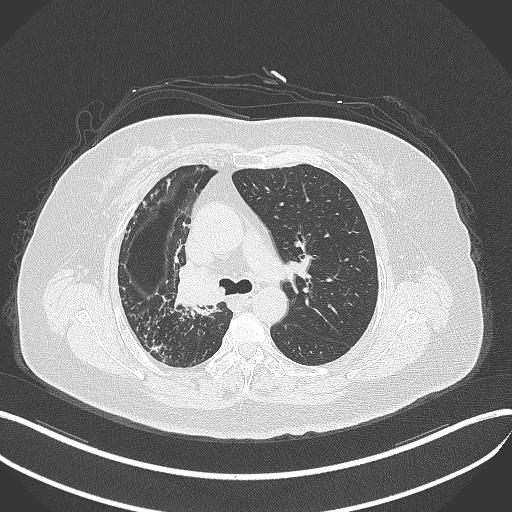
Chest CT, one axial slice. Position 236 of 376 along the scan axis. Lung window (W 1500 / L -600 HU). 1 mm slice thickness. 512 × 512 image matrix, field of view 400 × 400 mm. Female patient, age 60 years. Case-level facts recorded for this patient, not image findings: clinical TNM (as recorded): T1c N0 M0.
Outlined on this slice (rectangle marked by the reading radiologist):
- lung tumour (recorded histology: squamous cell carcinoma): bounding box <170,263,229,311> (left, top, right, bottom; pixels)